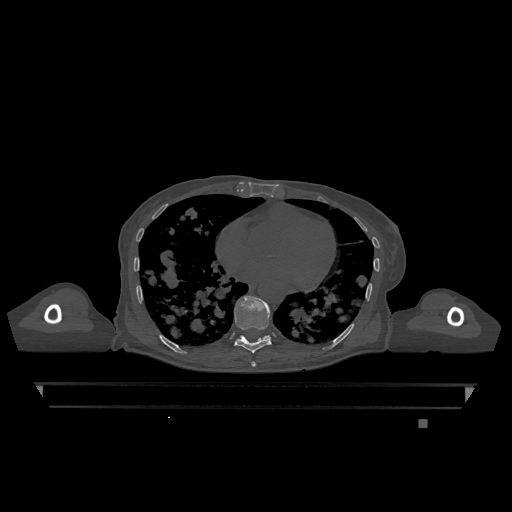
CT including the spine, one axial slice; bone window (W 1800 / L 400 HU); 0.5 mm slice thickness; 512 × 512 image matrix. Patient: female, 74 years. Case-level facts recorded for this patient, not image findings: primary cancer: lung.
Annotated regions visible in this slice (semi-automatic segmentation, software-assisted and operator-edited):
- T10 vertebra: bounding box (x1, y1, x2, y2) in pixels: (263, 335, 270, 339)
- T7 vertebra: (251, 361, 256, 367)
- T9 vertebra: (234, 296, 272, 353)